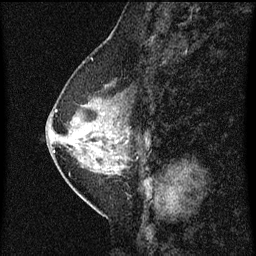
Breast MRI (dynamic contrast-enhanced), one sagittal slice. Slice 26 of 60 in the series (ordered by position). Dynamic contrast-enhanced series, image 2 of 3 at this slice position (ordered by acquisition). 1.5 T. TE 4.2 ms, TR 8 ms. 2 mm slice thickness. 256 × 256 image matrix. Patient: female, 47 years.
Outlined on this slice (semi-automatic segmentation, software-assisted and operator-edited):
- analysis volume of interest (the breast-tissue region the enhancement analysis was run in; not a lesion): bounding box <54,80,147,187> (left, top, right, bottom; pixels)
- tumour enhancement mask (voxels above the 70 % enhancement threshold inside the analysis volume of interest): <54,110,128,161>